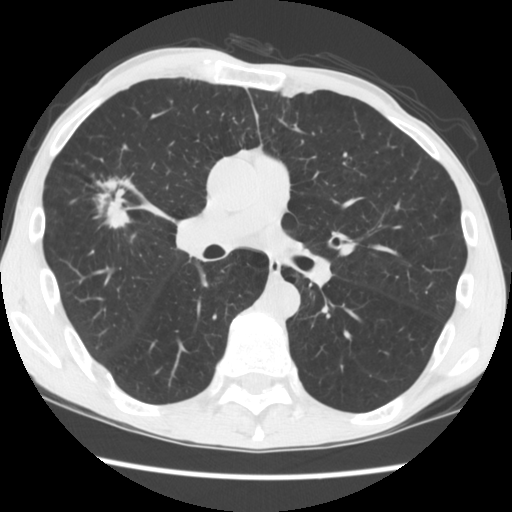
Low-dose screening chest CT, one axial slice; position 97 of 181 along the scan axis; 120 kVp; lung window (W 1500 / L -600 HU); 512 × 512 image matrix, field of view 330 × 330 mm.
Structures marked on this image (manually delineated by an expert):
- lesion 1 (tumor, upper lobe of right lung): bounding box (x1, y1, x2, y2) in pixels: (94, 179, 131, 229)